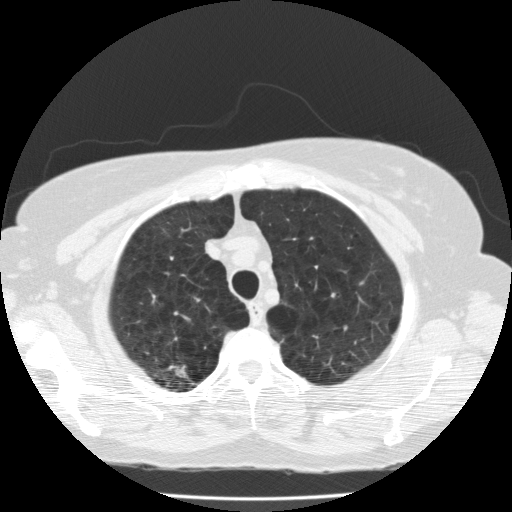
Chest CT (low-dose screening protocol), one axial image, second annual screen, lung window (W 1500 / L -600 HU), 2 mm slice thickness, standard (soft-tissue) reconstruction kernel (FC10), 120 kVp, slice 30 of 174 in the series, 512 × 512 image matrix, field of view 337 × 337 mm. Female participant, aged 59 years at enrolment. Current smoker at enrolment.
Lesion marked by an expert reader, bounding box (x1, y1, x2, y2) in pixels: (147, 355, 207, 399). Reader record for this screening exam (exam-level; its link to the box is not recorded): non-calcified nodule or mass ≥4 mm, right upper lobe, 11 × 6 mm, spiculated (stellate) margins, soft tissue attenuation, pre-existing on the prior screen: yes; interval growth: no. Official screen result: positive, no significant change: stable abnormalities potentially related to lung cancer, unchanged since the prior screening exam. Participant outcome: lung cancer diagnosed 490 days after this screen (after the third annual screen) — adenocarcinoma, NOS, right upper lobe, poorly differentiated (G3), stage IA (AJCC 6th edition), 20 mm at pathology.